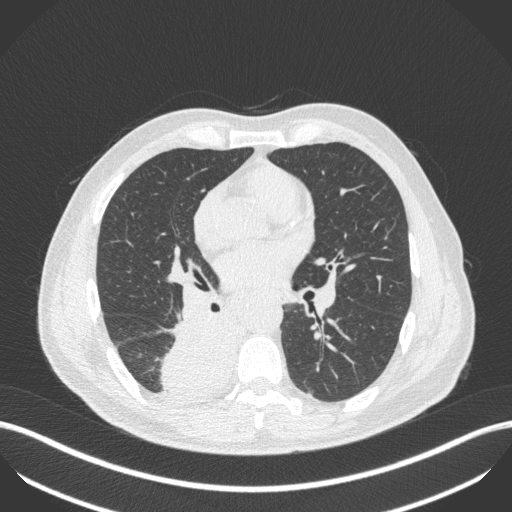
Chest CT, one axial slice. Position 244 of 451 along the scan axis. 100 kVp. Lung window (W 1500 / L -600 HU). 1 mm slice thickness. 512 × 512 image matrix. Patient: male, 61 years. Case-level facts recorded for this patient, not image findings: clinical TNM (as recorded): T1 N0 M0.
Annotated regions visible in this slice (rectangle marked by the reading radiologist):
- lung tumour (recorded histology: small cell carcinoma): bounding box (x1, y1, x2, y2) in pixels: (151, 307, 239, 394)